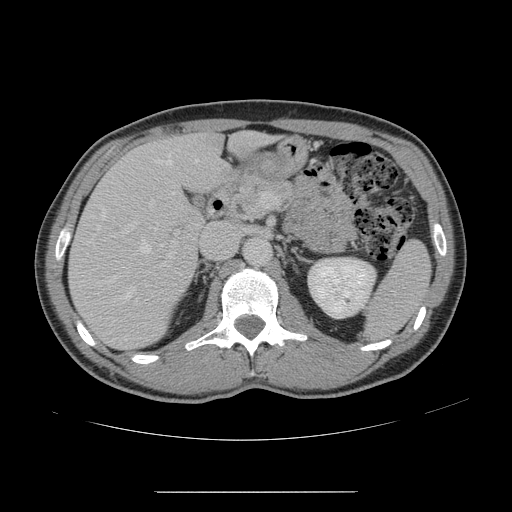
Contrast-enhanced abdominal CT, one axial slice; 120 kVp; intravenous contrast given; soft-tissue window (W 400 / L 40 HU); 2.5 mm slice thickness; 512 × 512 image matrix. Male patient, age 53 years. From the clinical record (not read from this slice): diagnosis: colorectal cancer liver metastases, imaged before liver resection; multiple liver metastases: yes; largest metastasis: 2.4 cm; chemotherapy before resection: yes.
Outlined on this slice (manually delineated by an expert):
- hepatic veins: bounding box (x1, y1, x2, y2) in pixels: (98, 159, 198, 302)
- liver: (70, 132, 270, 349)
- planned liver remnant (the part of the liver to remain after resection): (156, 133, 270, 191)
- portal vein (with intrahepatic branches): (129, 192, 267, 268)